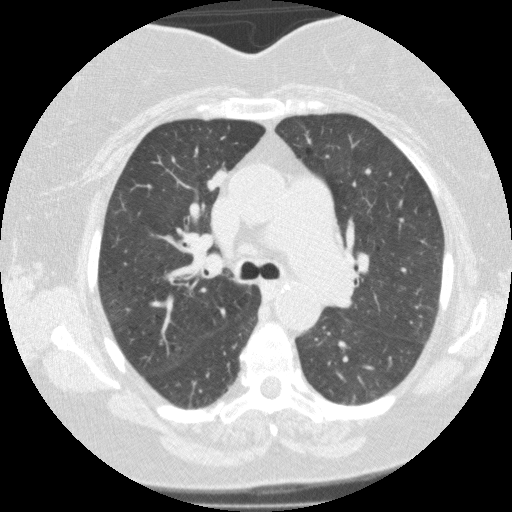
Low-dose screening chest CT, one axial slice. Slice 94 of 146 in the series (ordered by position). 120 kVp. Lung window (W 1500 / L -600 HU). 2 mm slice thickness. 512 × 512 image matrix, field of view 330 × 330 mm.
Annotated regions visible in this slice (expert manual segmentation):
- lesion 2 (tumor, upper lobe of right lung): bounding box <206,170,229,191> (left, top, right, bottom; pixels)